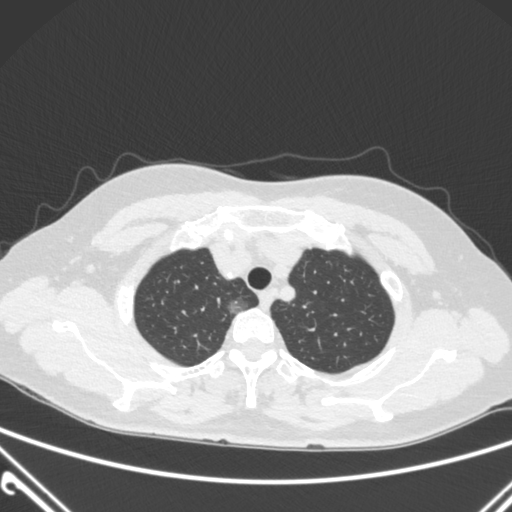
Chest CT, one axial slice; slice 240 of 300 in the series (ordered by position); lung window (W 1500 / L -600 HU); 512 × 512 image matrix. Female patient, age 54 years. Case-level facts recorded for this patient, not image findings: clinical TNM (as recorded): T1a N0 M0.
Structures marked on this image (bounding box drawn by a radiologist):
- lung tumour (recorded histology: adenocarcinoma): bounding box <220,291,255,317> (left, top, right, bottom; pixels)